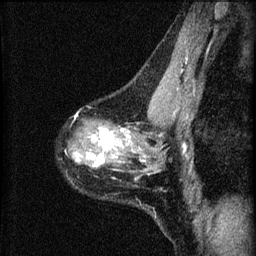
Breast MRI (dynamic contrast-enhanced), one sagittal slice; slice 39 of 60 in the series (ordered by position); dynamic contrast-enhanced series, image 2 of 4 at this slice position (ordered by acquisition); 1.5 T; TE 4.2 ms, TR 8.2 ms; 2 mm slice thickness; 256 × 256 image matrix. Patient: female, 41 years.
Annotated regions visible in this slice (semi-automatically segmented with operator editing):
- analysis volume of interest (the breast-tissue region the enhancement analysis was run in; not a lesion): bounding box [x1, y1, x2, y2] px = [69, 91, 166, 210]
- tumour enhancement mask (voxels above the 70 % enhancement threshold inside the analysis volume of interest): [75, 128, 131, 166]